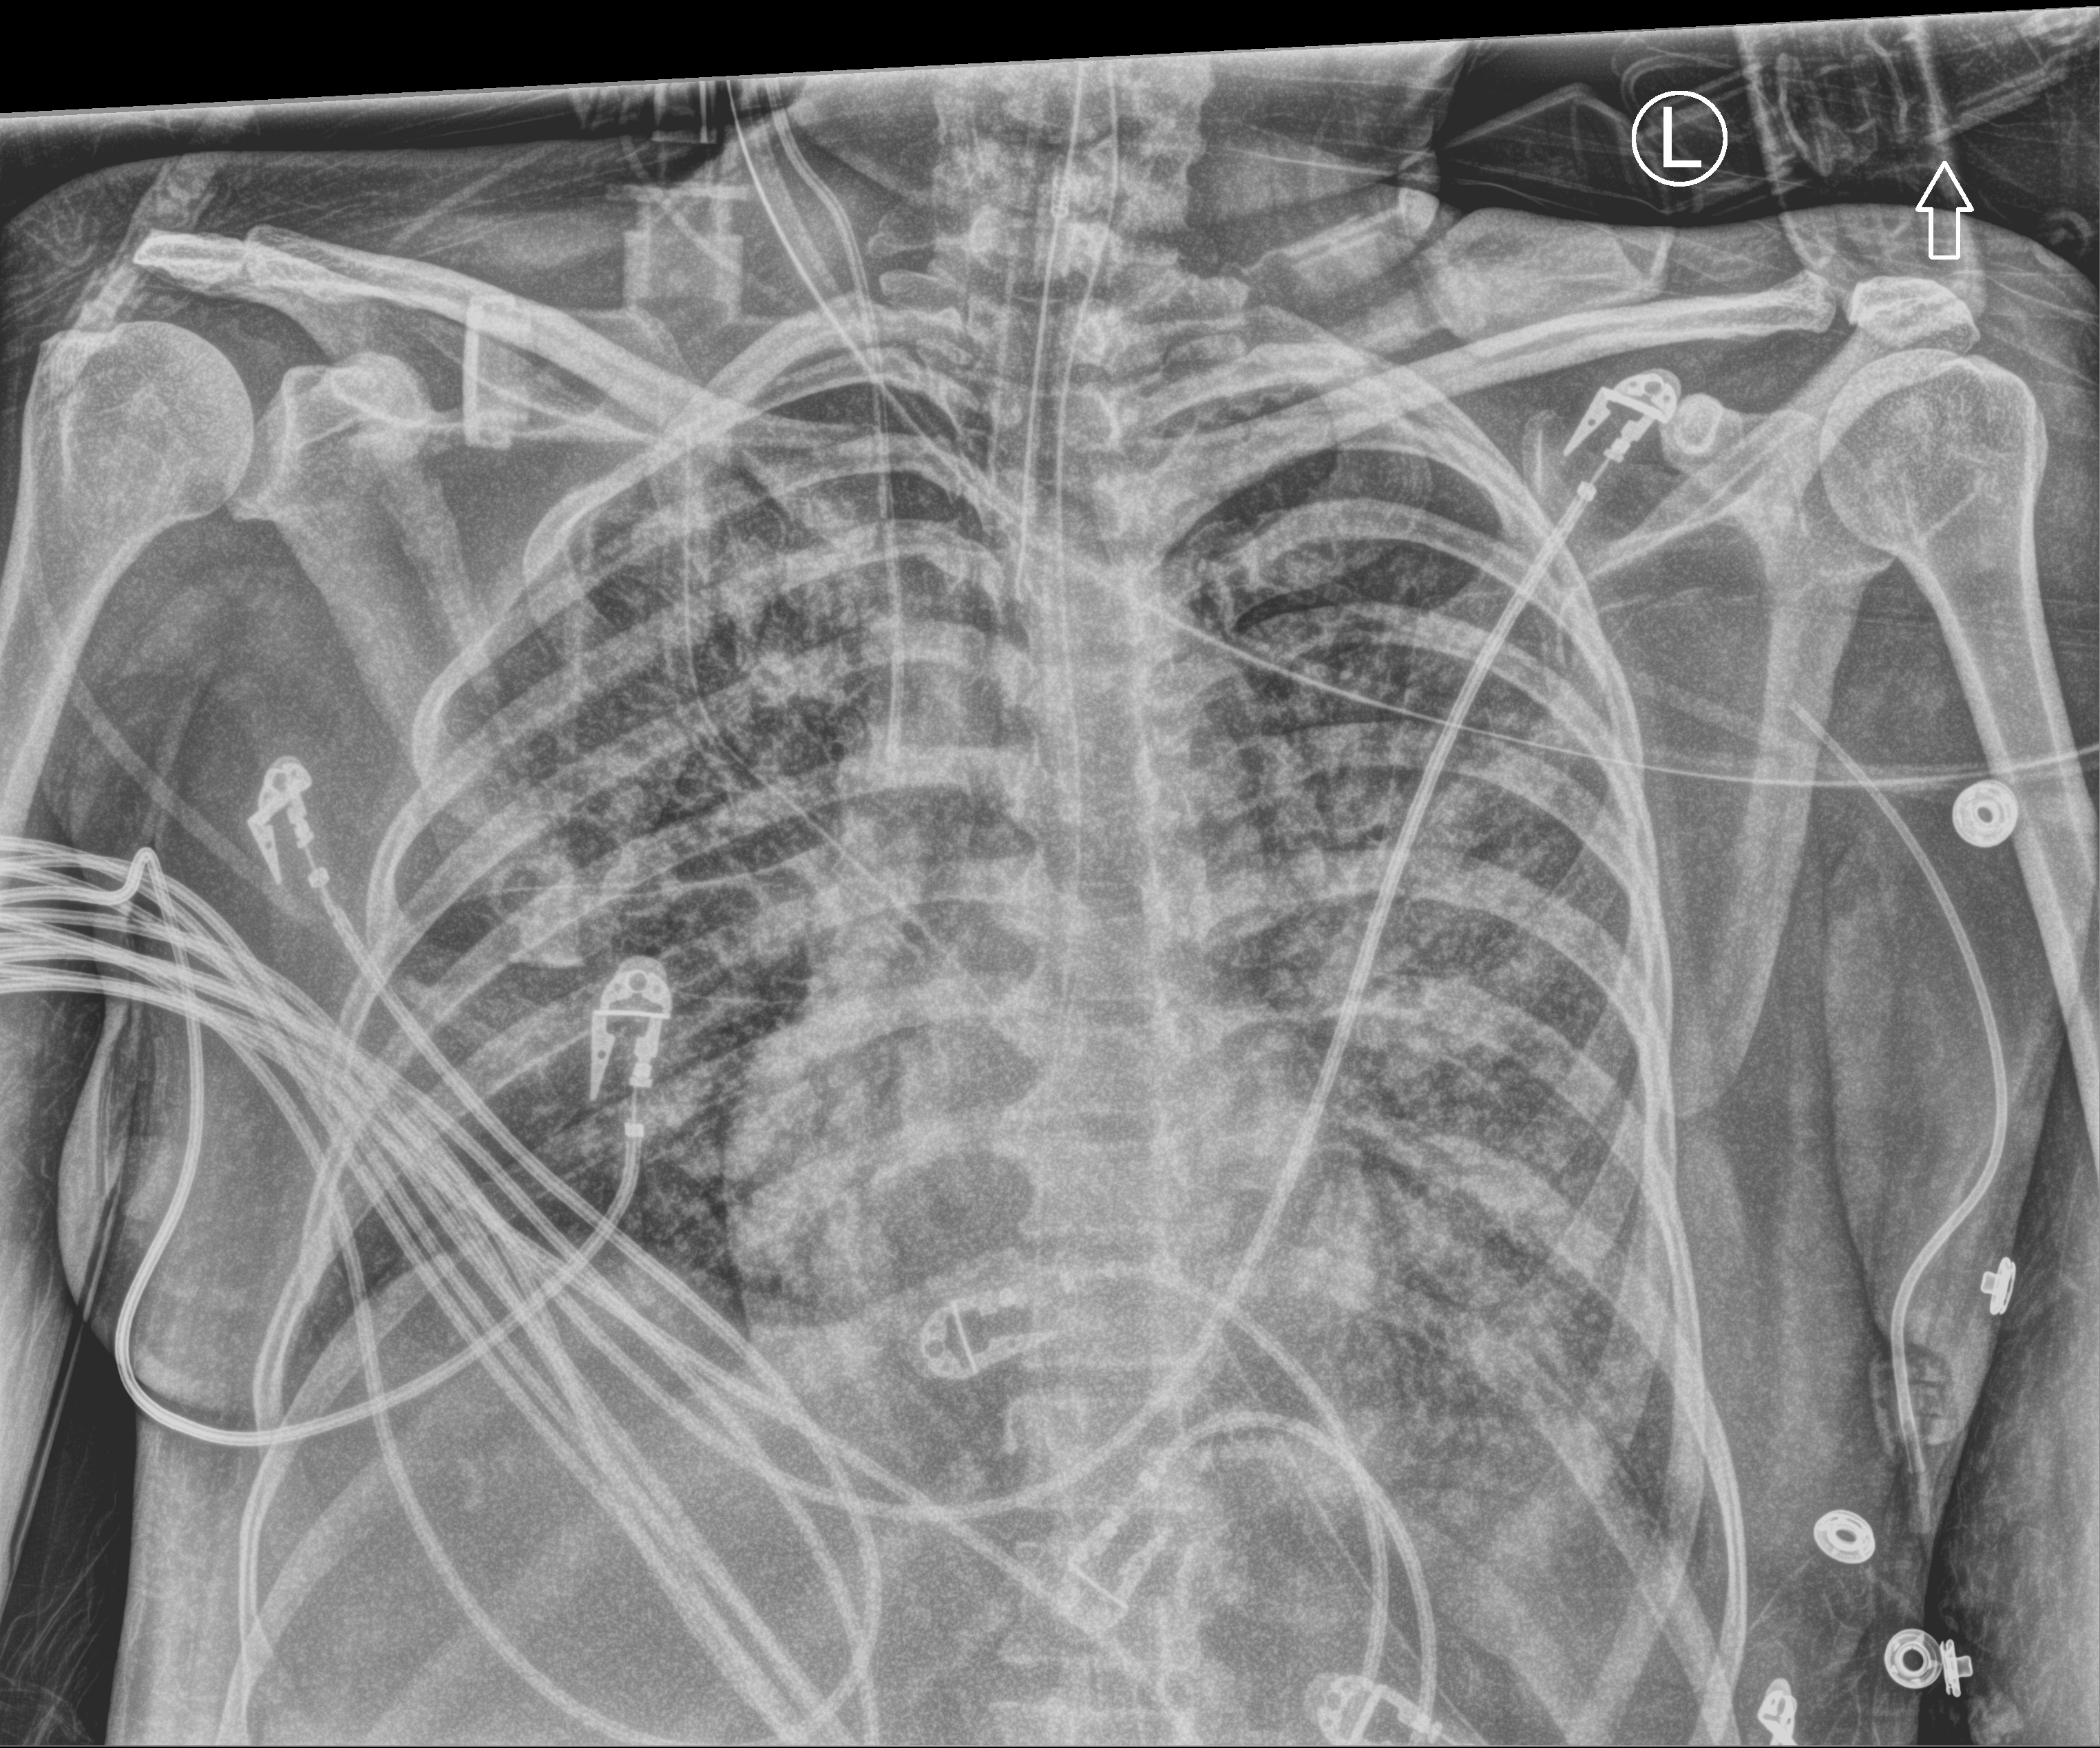
Chest X-ray (portable). Patient hospitalised with COVID-19; female, aged 18–59 years.
Hospital-stay facts (about this admission, not read from this image; timing relative to this image not recorded): admitted to intensive care during this hospital stay: yes.